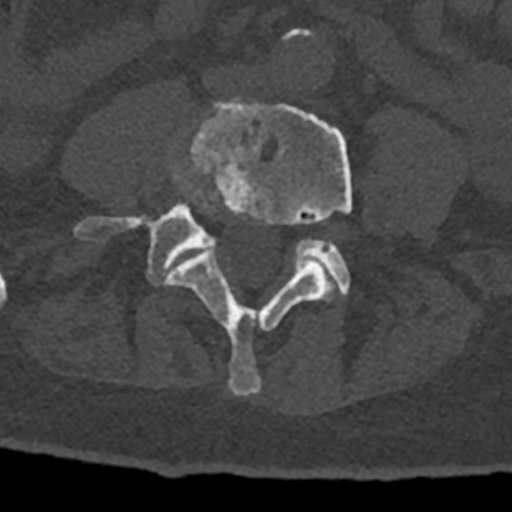
CT including the spine, one axial slice. Slice 237 of 797 in the series (ordered by position). Reconstruction kernel Br40s/3. 120 kVp. Bone window (W 1800 / L 400 HU). 512 × 512 image matrix, field of view 160 × 160 mm. Patient: male, 74 years. From the clinical record (not read from this slice): primary cancer: renal.
Annotated regions visible in this slice (semi-automatically segmented with operator editing):
- L4 vertebra: bounding box (x1, y1, x2, y2) in pixels: (166, 99, 352, 395)
- L5 vertebra: (74, 203, 350, 294)